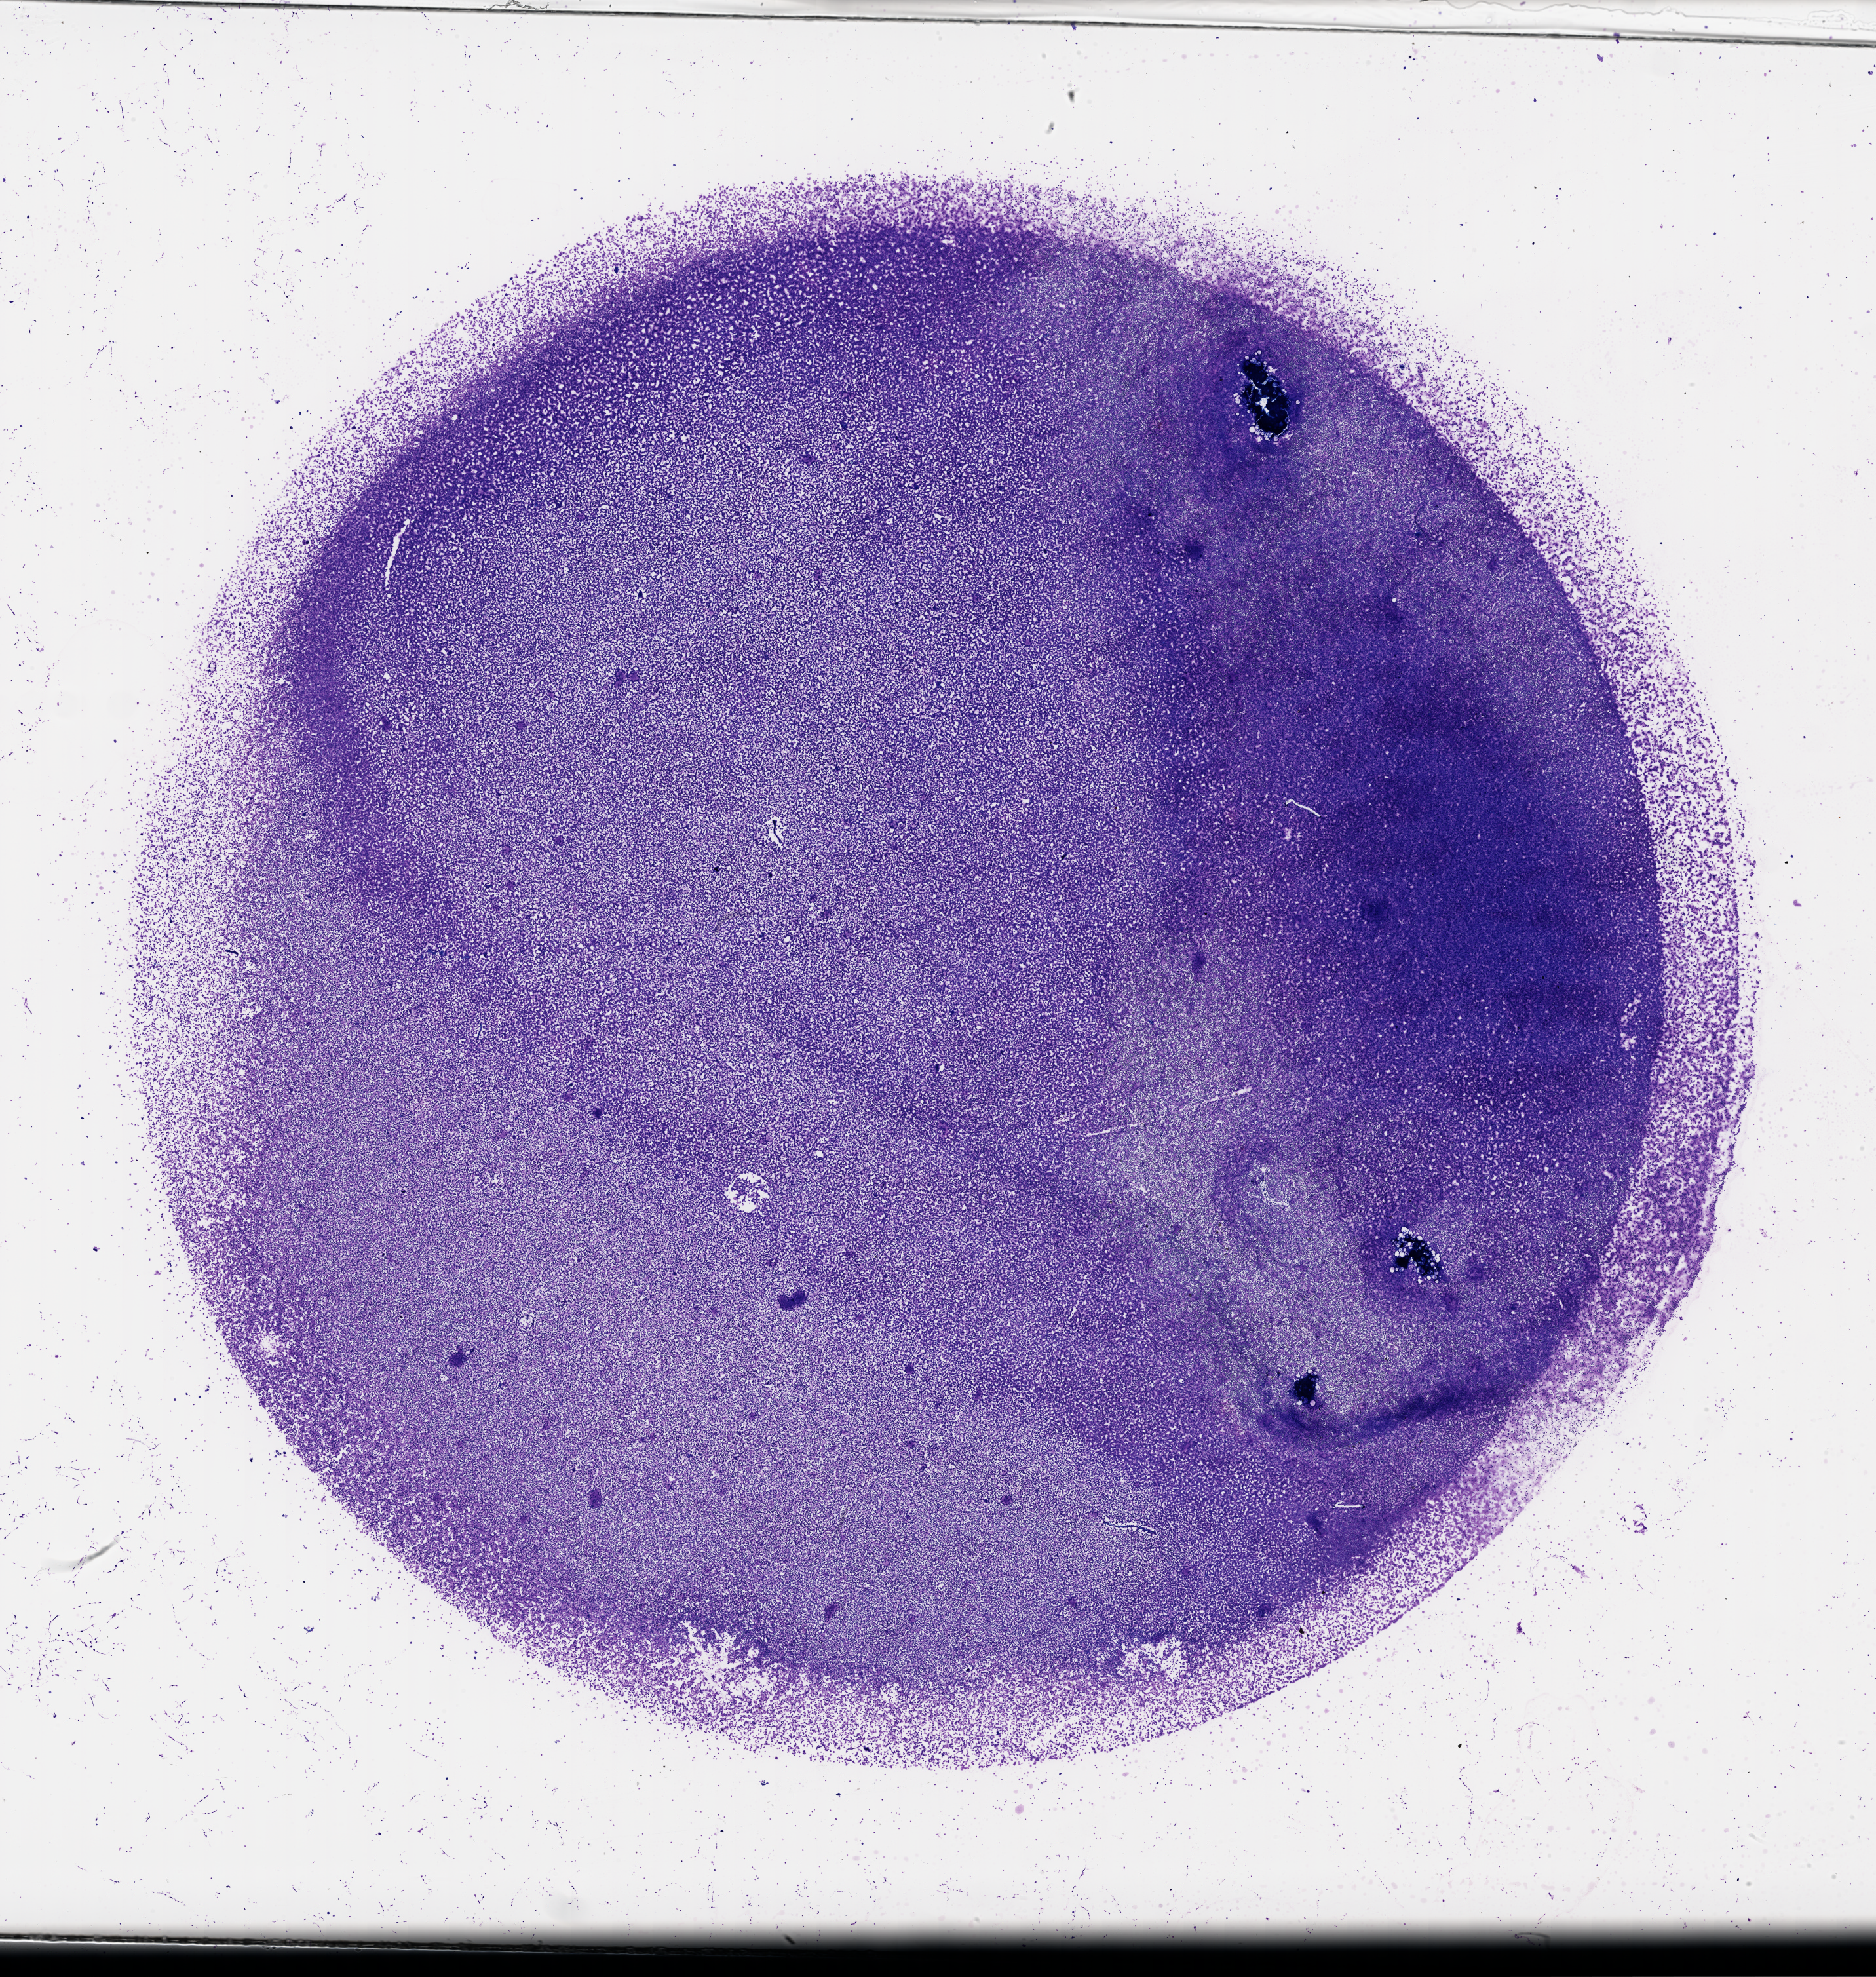
H&E whole-slide image — a low-resolution overview of the entire scanned area, about 23.1 x 24.4 mm (acquisition: 40x scan), bone marrow (leukaemic) sample. Patient: male, age 60 years. Blasts: 40%.
FAB classification: M2. WHO classification: AML with maturation. Diagnosis: Acute Myeloid Leukemia.